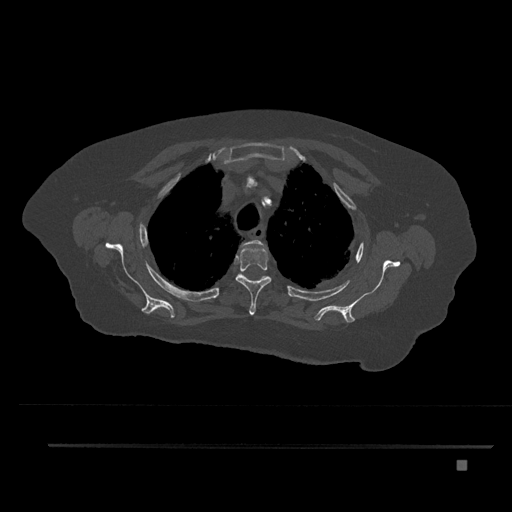
CT including the spine, one axial slice. Position 634 of 797 along the scan axis. Bone window (W 1800 / L 400 HU). 0.5 mm slice thickness. 512 × 512 image matrix. Female patient, age 76 years. From the clinical record (not read from this slice): primary cancer: lung; vertebrae with lytic lesions (as recorded): T11, L3.
Outlined on this slice (semi-automatic segmentation, software-assisted and operator-edited):
- T2 vertebra: bounding box <241,240,265,246> (left, top, right, bottom; pixels)
- T3 vertebra: <235,248,272,315>
- T4 vertebra: <240,273,264,277>